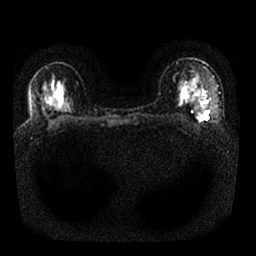
Breast MRI, one axial slice; position 16 of 25 along the scan axis; diffusion-weighted series; image 2 of 4 stored at this slice position (different b-values; order by instance number); 1.5 T; 256 × 256 image matrix, field of view 330 × 330 mm. Female patient.
Annotated regions visible in this slice (manually delineated by an expert):
- tumour on diffusion-weighted imaging: bounding box [x1, y1, x2, y2] px = [196, 111, 205, 121]